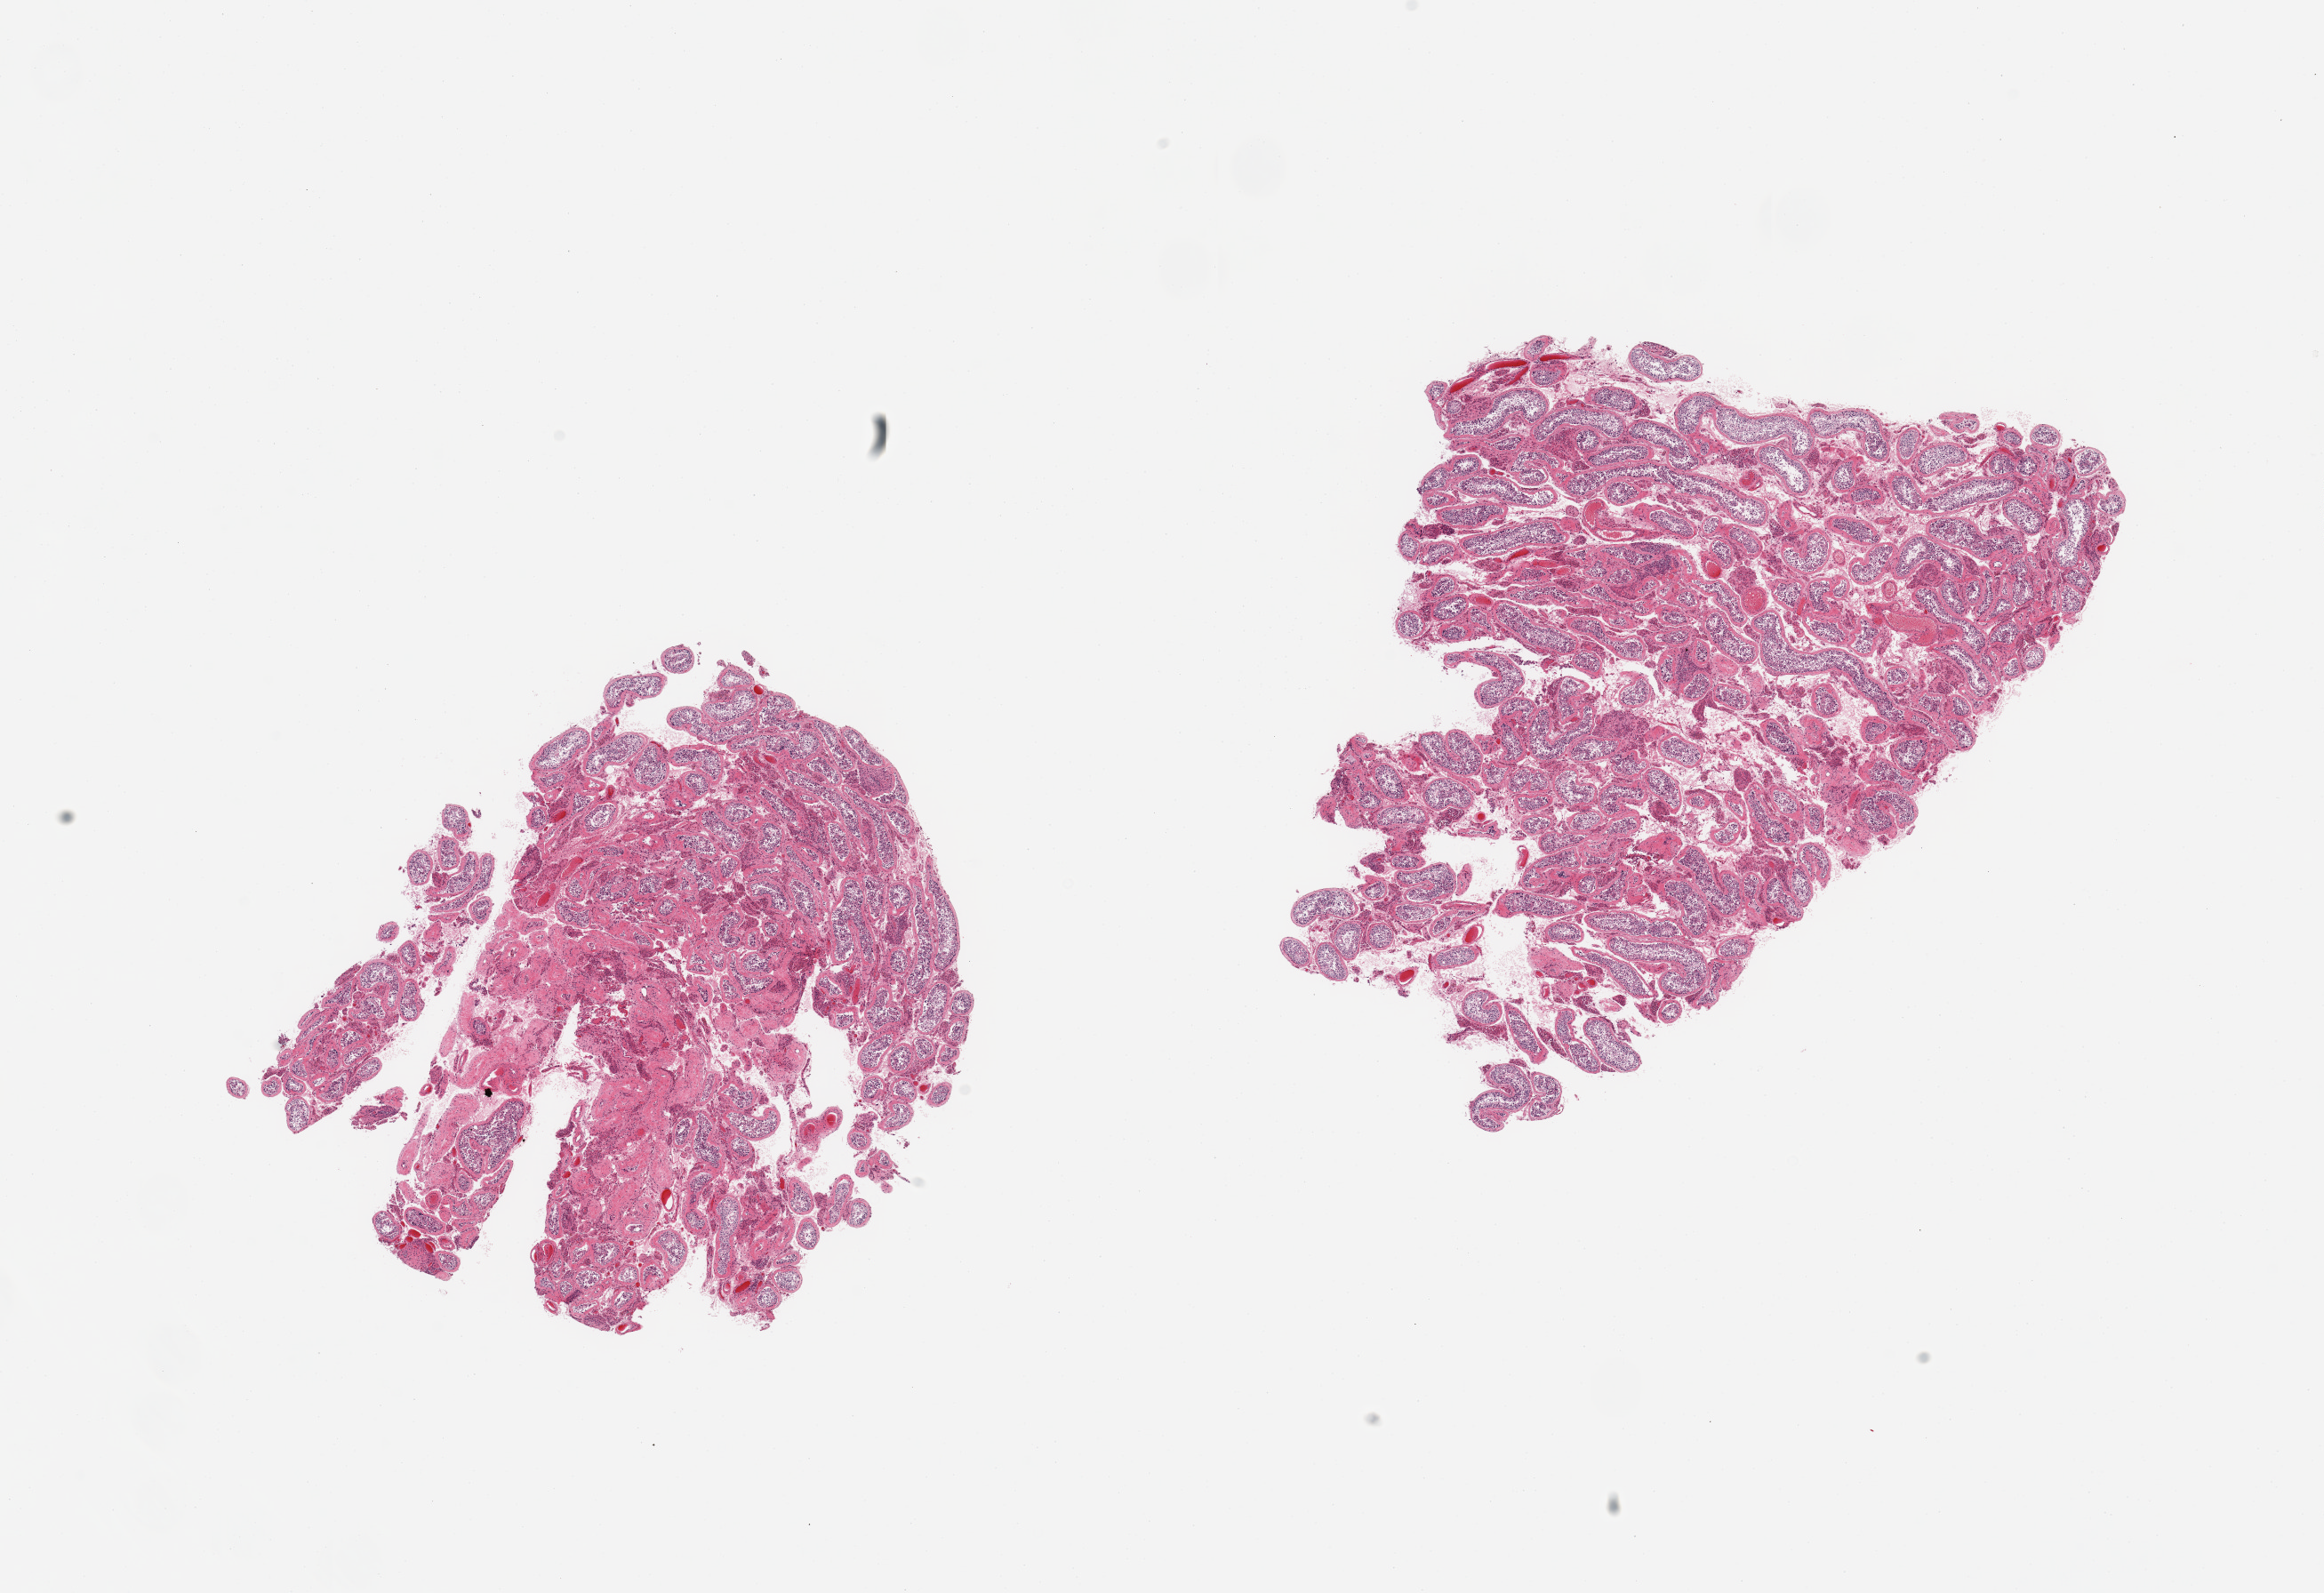
H&E whole-slide image — shown as a low-resolution overview of the whole scanned area (about 20.7 x 14.2 mm, from a 20x scan); PAXgene-fixed, paraffin-embedded tissue; sampled site (target tissue): testis; donor tissue sample. Male donor.
Pathologist's review note for this sample: 2 pieces; spermatogenesis; 3 mm scarred area; Leydig cell hyperplasia.